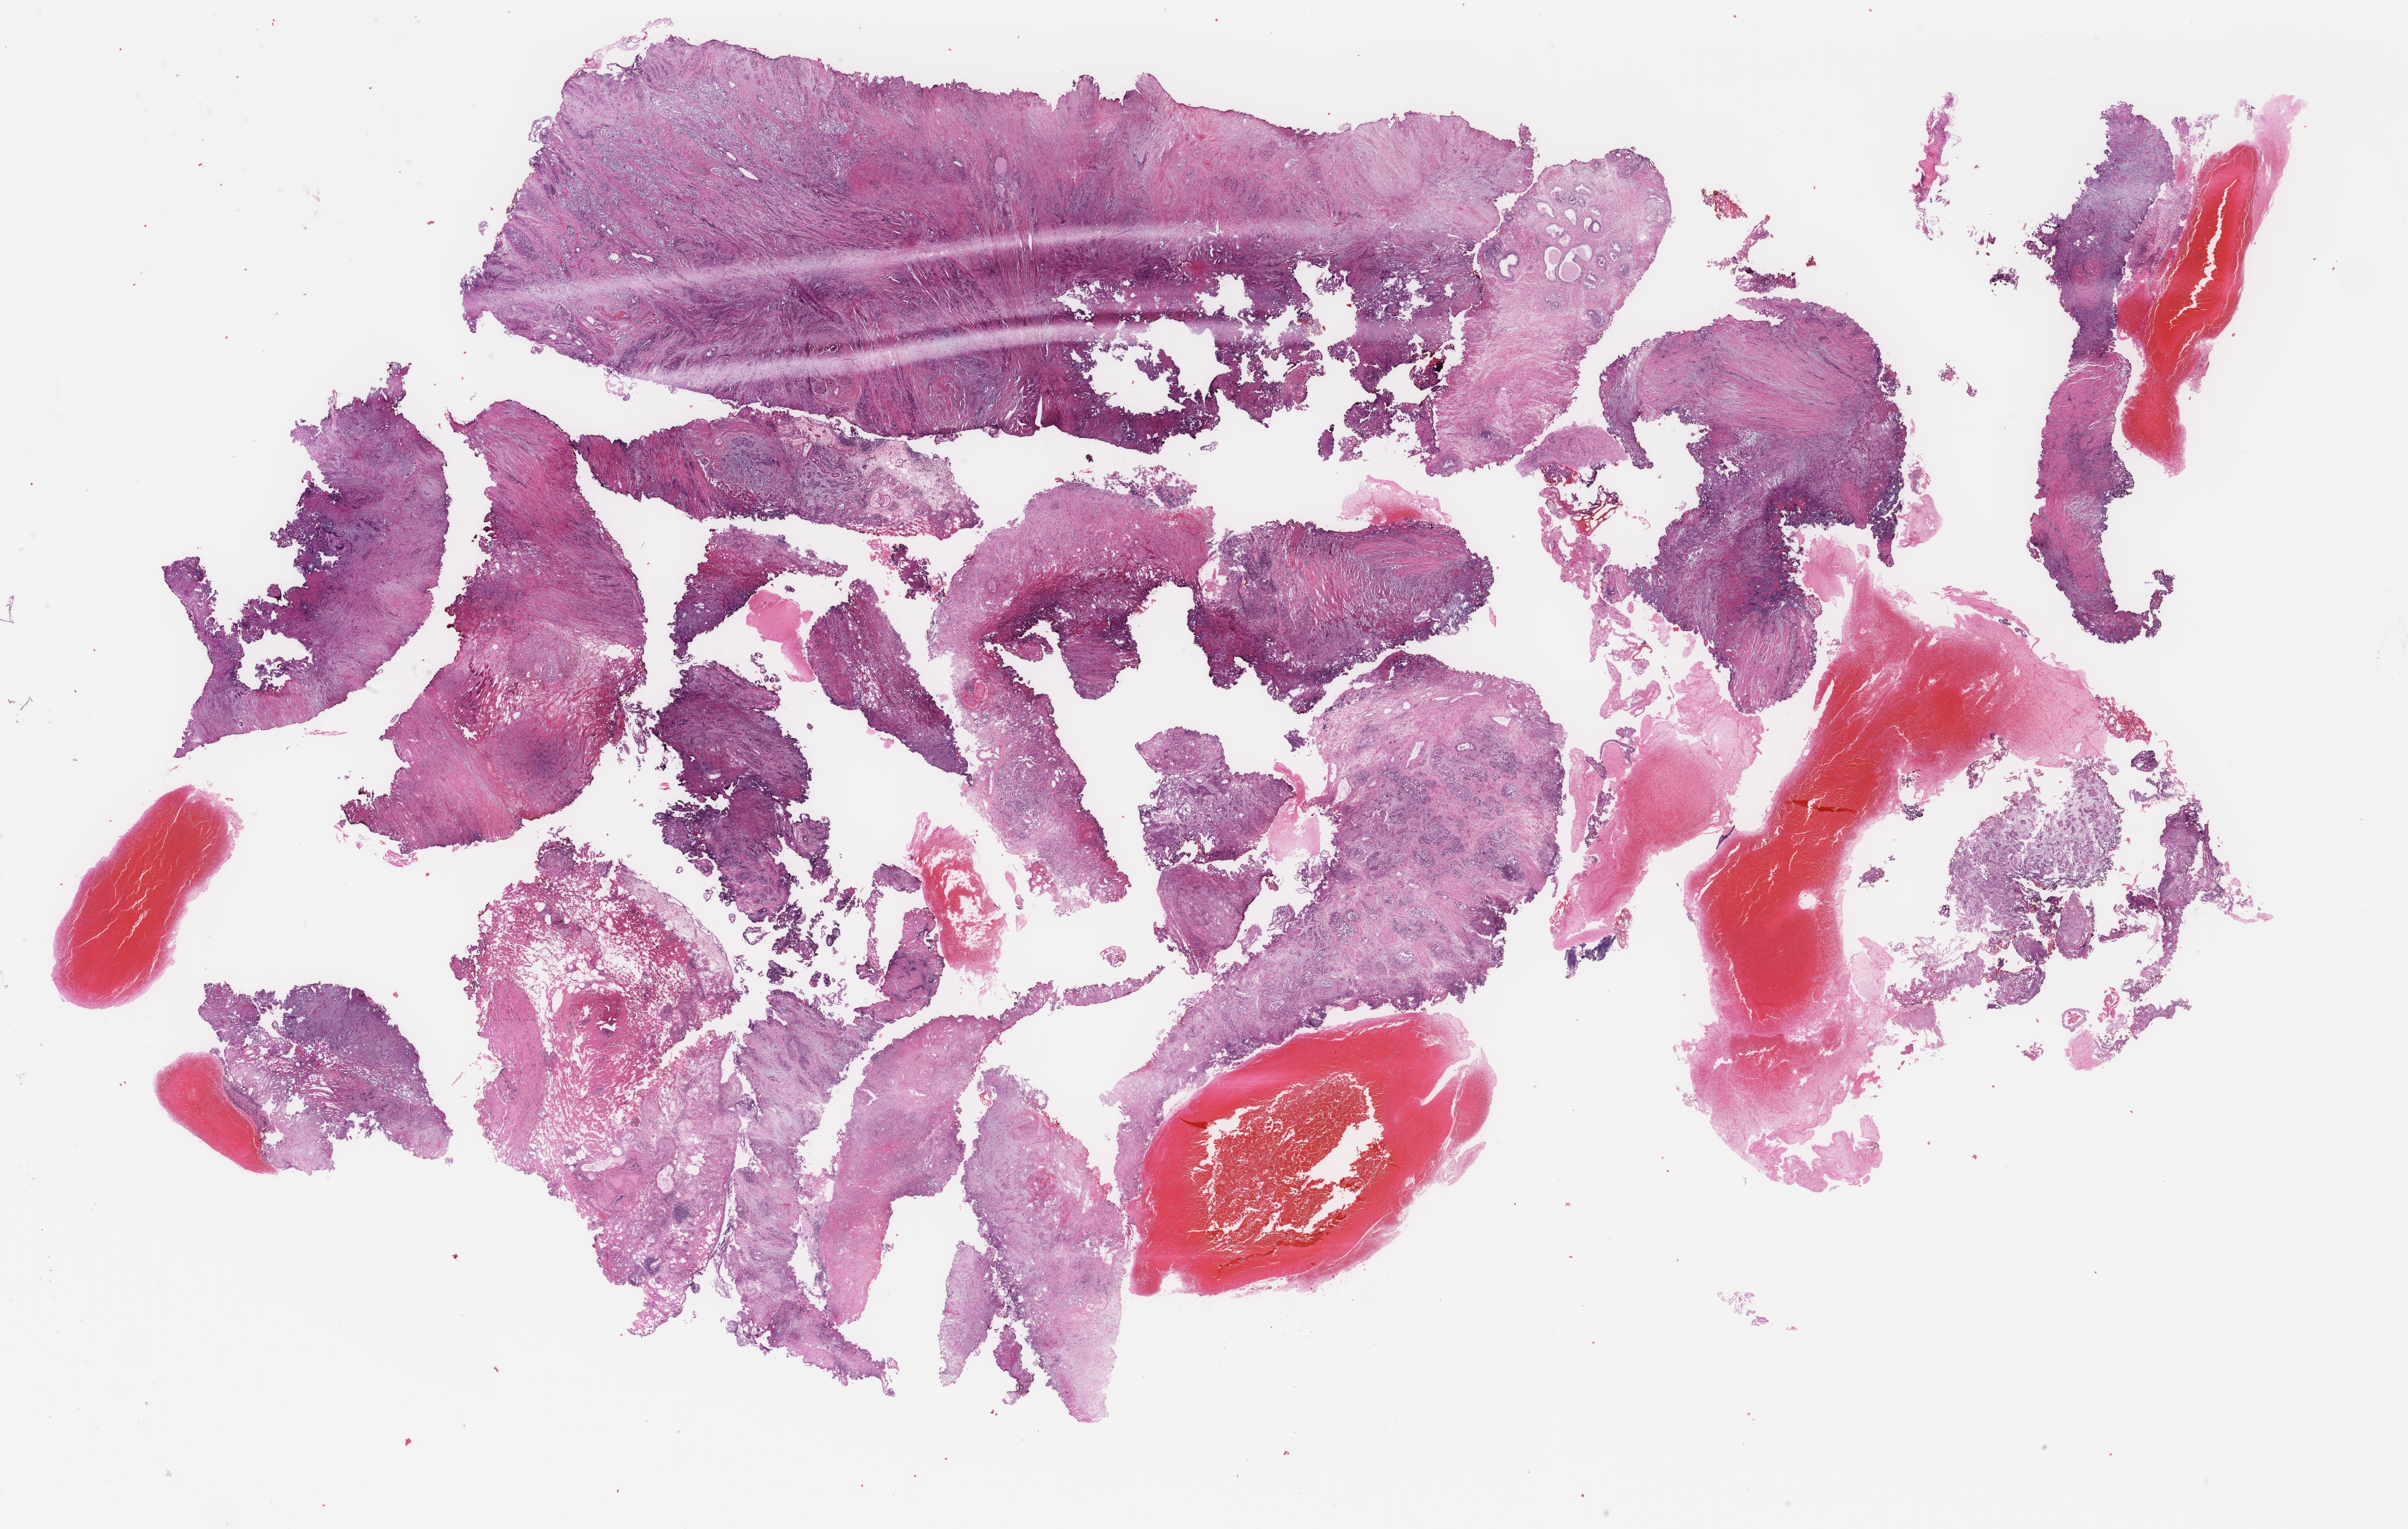
H&E whole-slide image — a low-resolution overview of the entire scanned area, about 31.2 x 19.8 mm (acquisition: 40x scan); formalin-fixed paraffin-embedded (FFPE) diagnostic section; bladder, primary tumour sample. Male, age 57 years at initial diagnosis. Histologic grade: high grade.
Histologic diagnosis: Transitional cell carcinoma. AJCC pathologic stage: II.